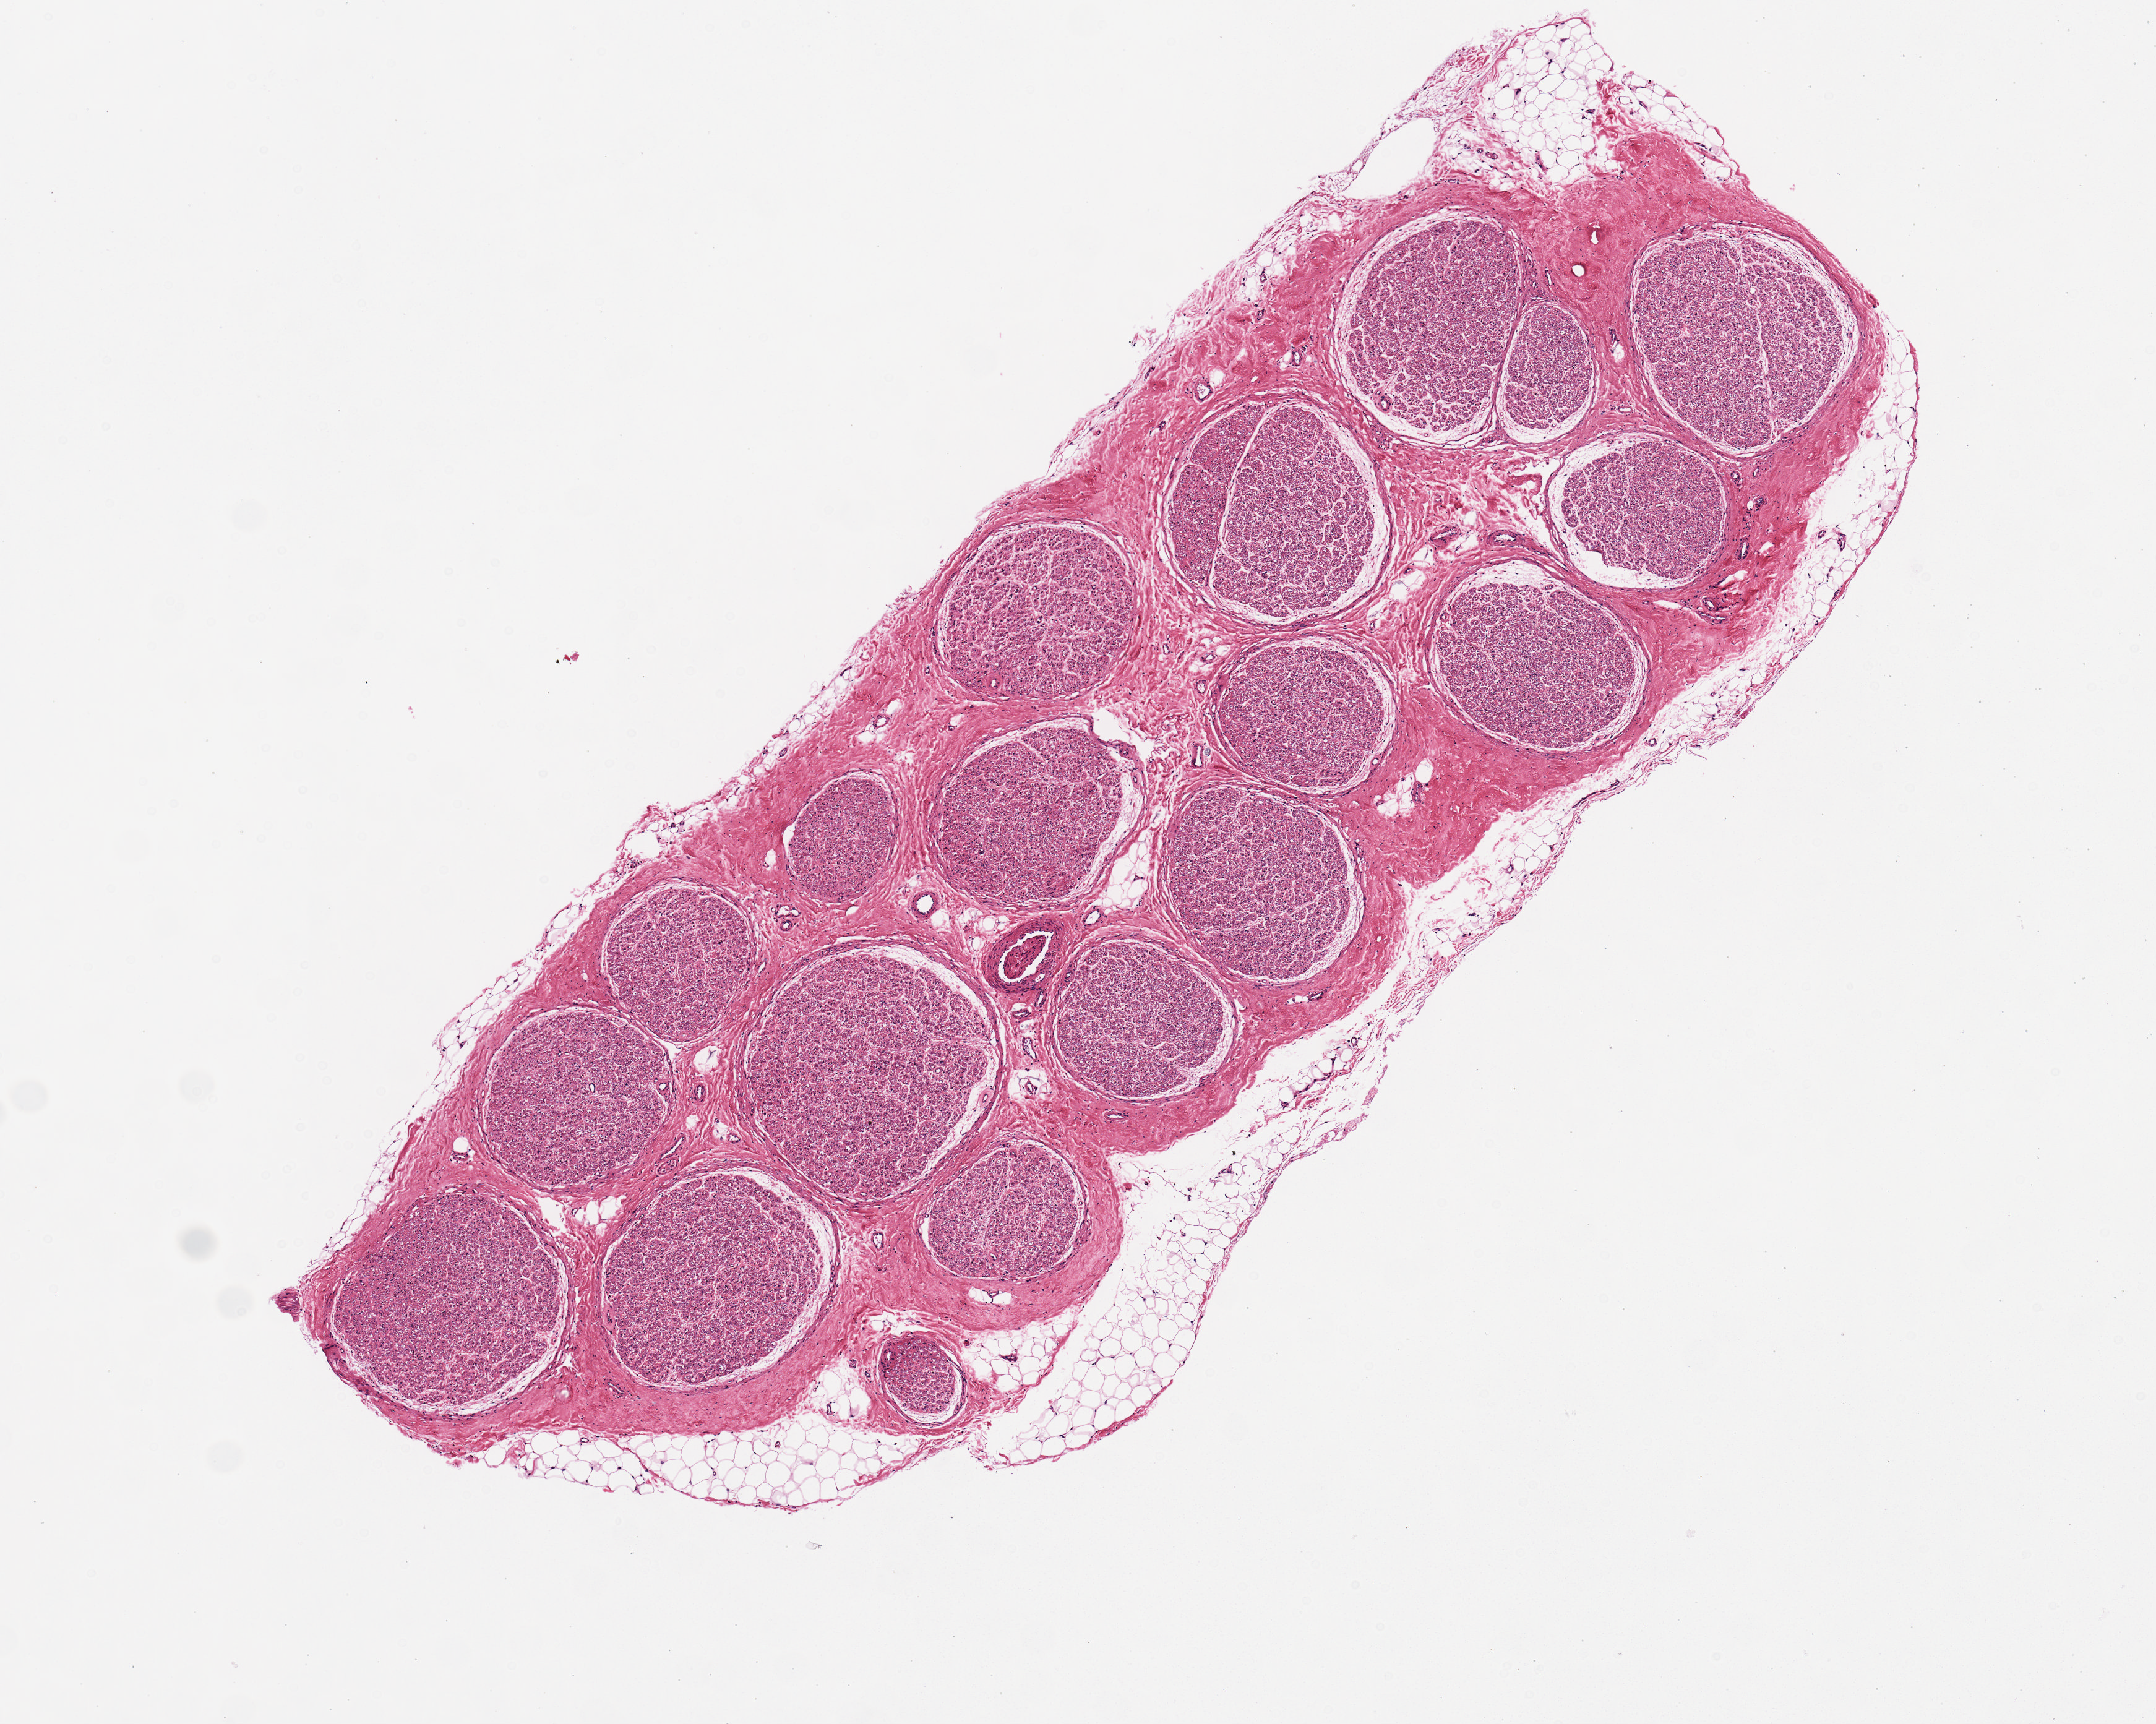
Haematoxylin and eosin whole-slide image — a low-resolution overview of the entire scanned area, about 6.9 x 5.5 mm. PAXgene-fixed, paraffin-embedded tissue. Section of tibial nerve (target tissue). Donor tissue sample. Donor sex: female.
* review note (as recorded): Contains 19 nerve bundles. <10% fat. 5.8x2mm